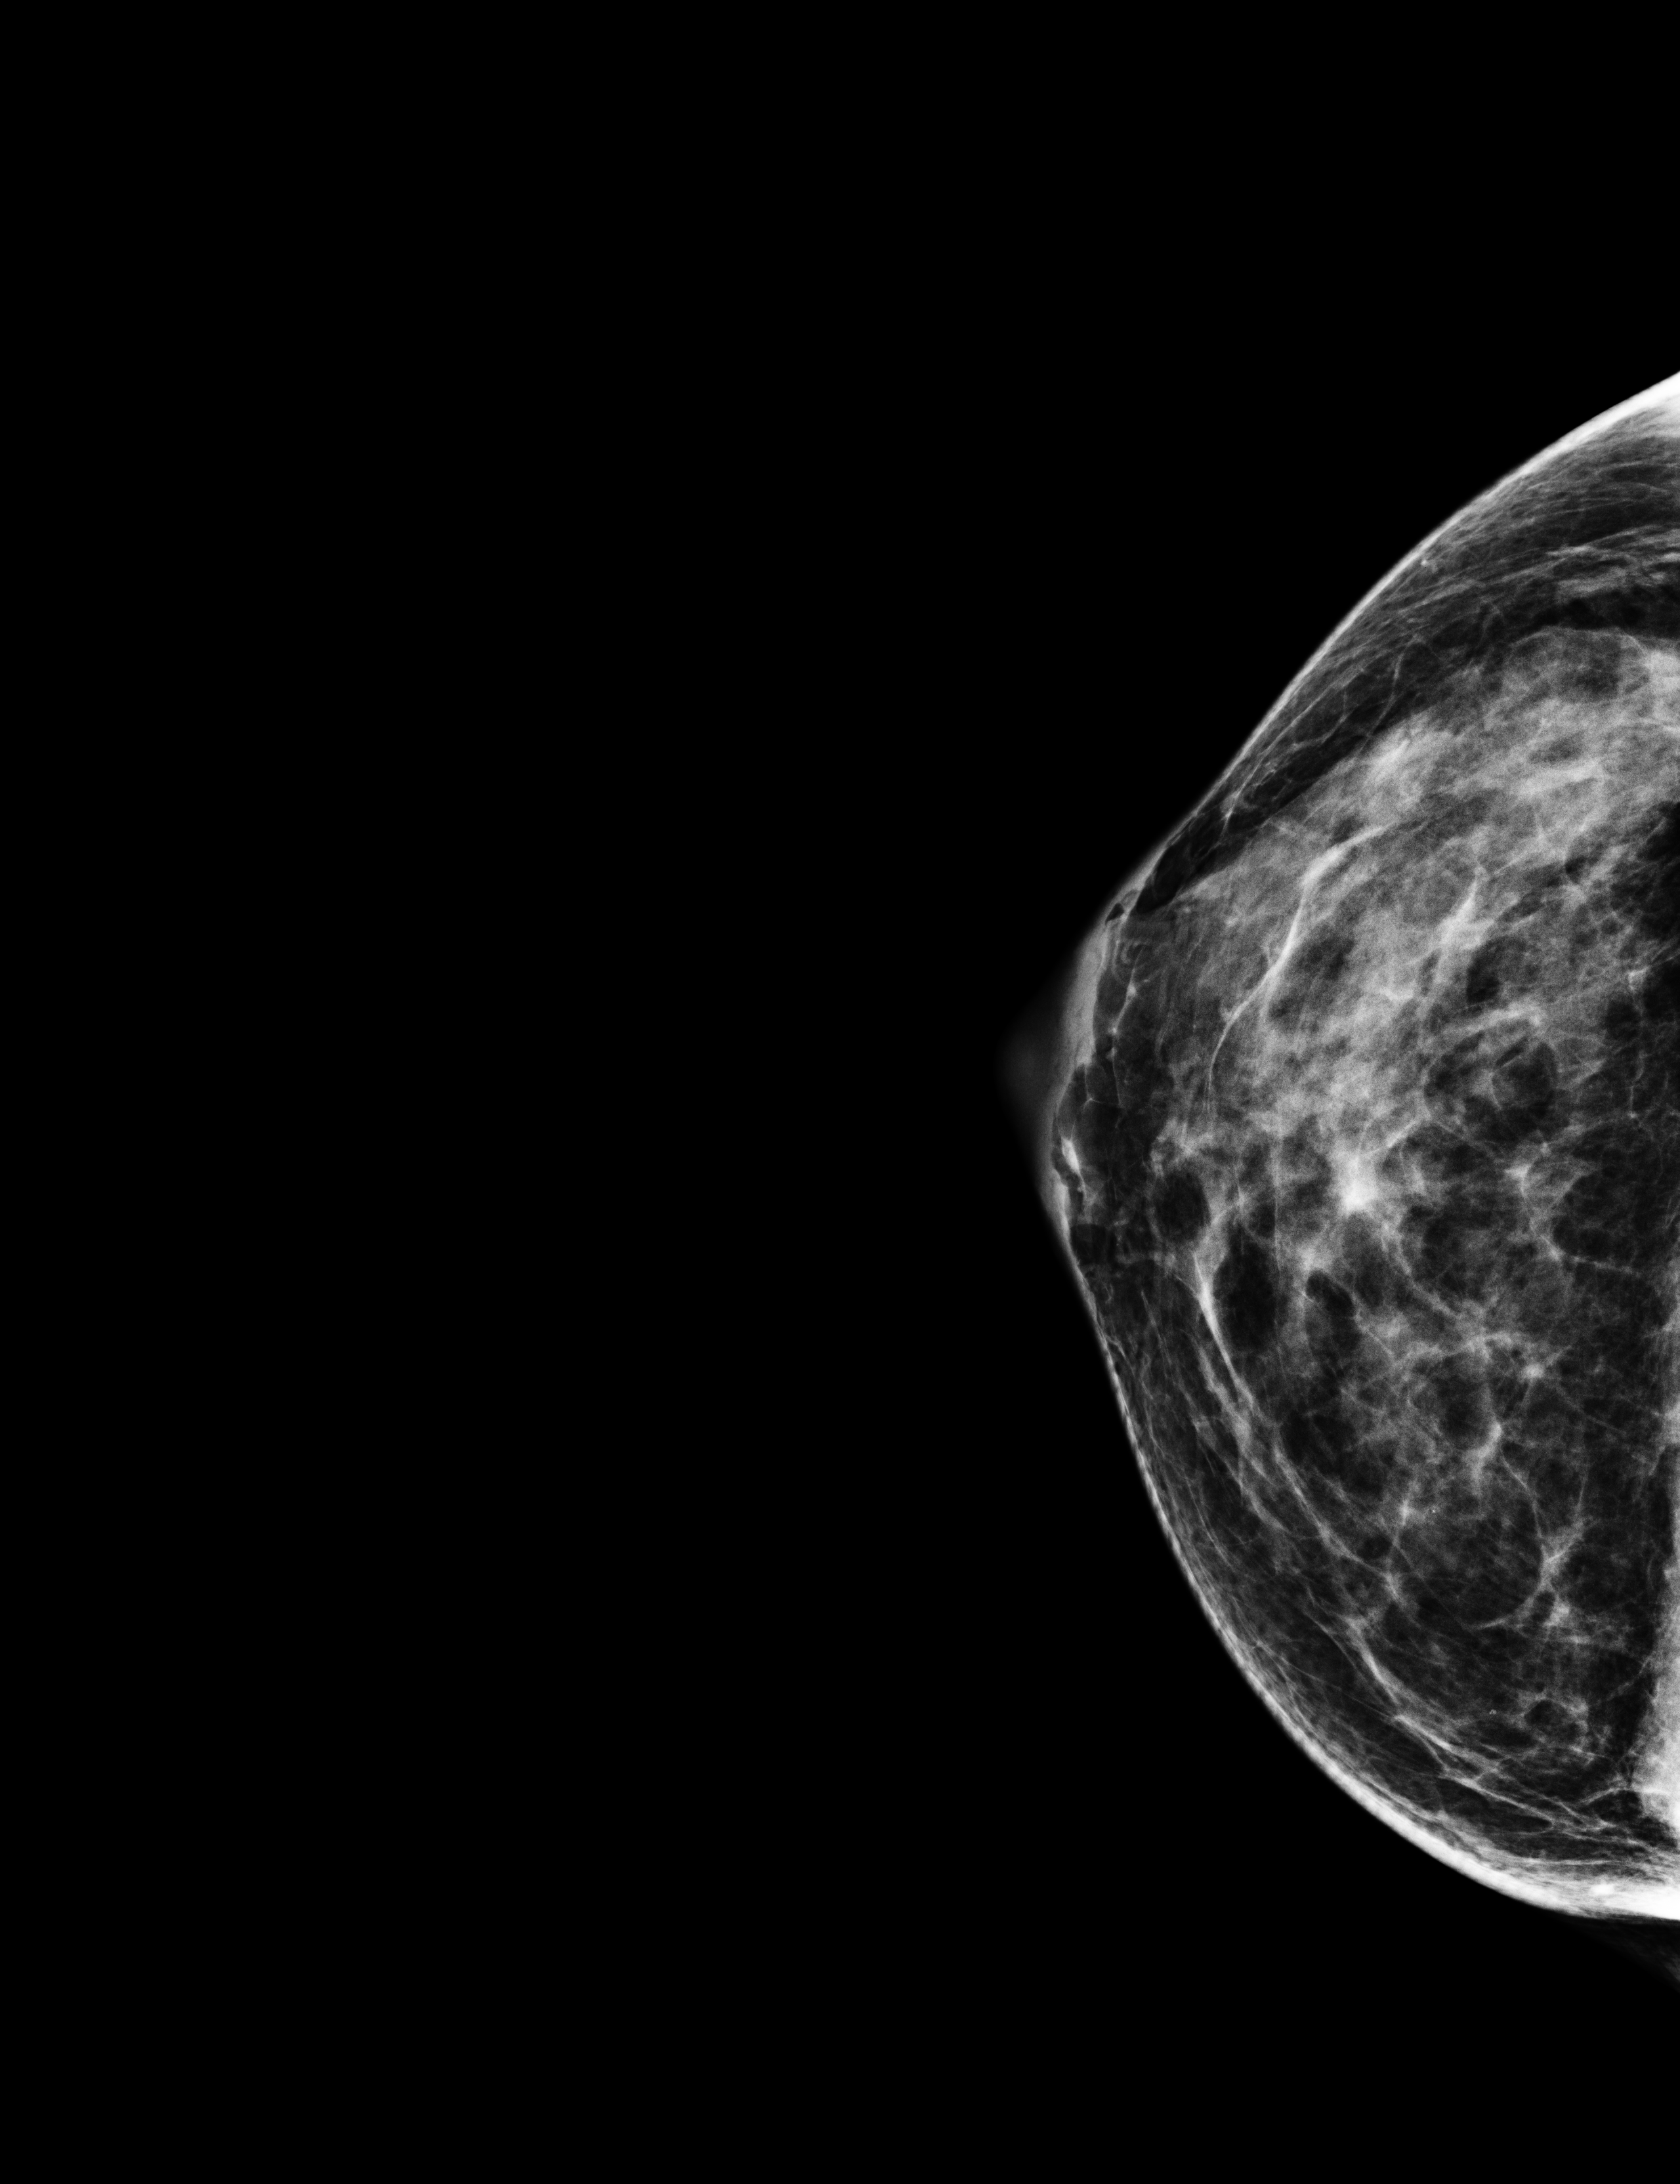
Digital mammogram (FFDM); right breast; CC view; annual screening mammography examination. Patient aged 51 years (female).
Breast density at the screening exam (both breasts): heterogeneously dense (BI-RADS density category c). Final BI-RADS assessment for this screening round (tomosynthesis exam, both breasts): category 1. Recall: no recall after this screen.